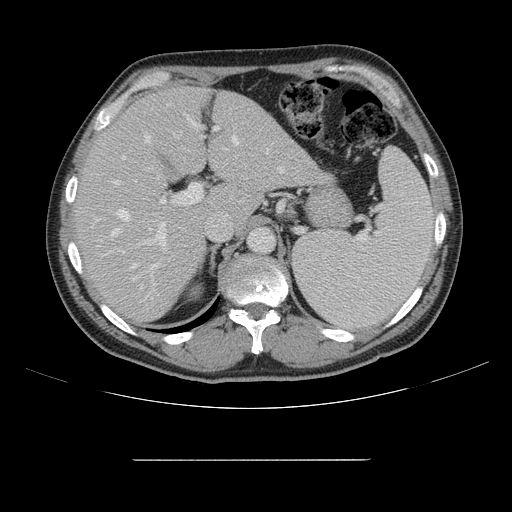
Contrast-enhanced abdominal CT, one axial slice; position 102 of 164 along the scan axis; soft-tissue window (W 400 / L 40 HU); 2.5 mm slice thickness; 512 × 512 image matrix, field of view 404 × 404 mm. Male patient, age 54 years. Case-level facts recorded for this patient, not image findings: diagnosis: colorectal cancer liver metastases, imaged before liver resection.
Annotated regions visible in this slice (outlined manually by an expert reader):
- hepatic veins: bounding box <111,136,284,269> (left, top, right, bottom; pixels)
- liver: <75,86,325,324>
- planned liver remnant (the part of the liver to remain after resection): <75,86,238,323>
- portal vein (with intrahepatic branches): <114,104,238,303>